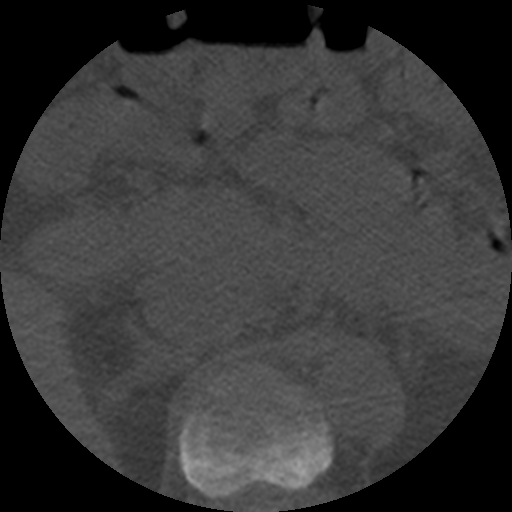
CT including the spine, one axial slice; reconstruction kernel STANDARD; 120 kVp; bone window (W 1800 / L 400 HU); 512 × 512 image matrix, field of view 160 × 160 mm. Patient age 57 years. Case-level facts recorded for this patient, not image findings: primary cancer: prostate.
Structures marked on this image (semi-automatic segmentation, software-assisted and operator-edited):
- T11 vertebra: bounding box (x1, y1, x2, y2) in pixels: (179, 389, 332, 499)